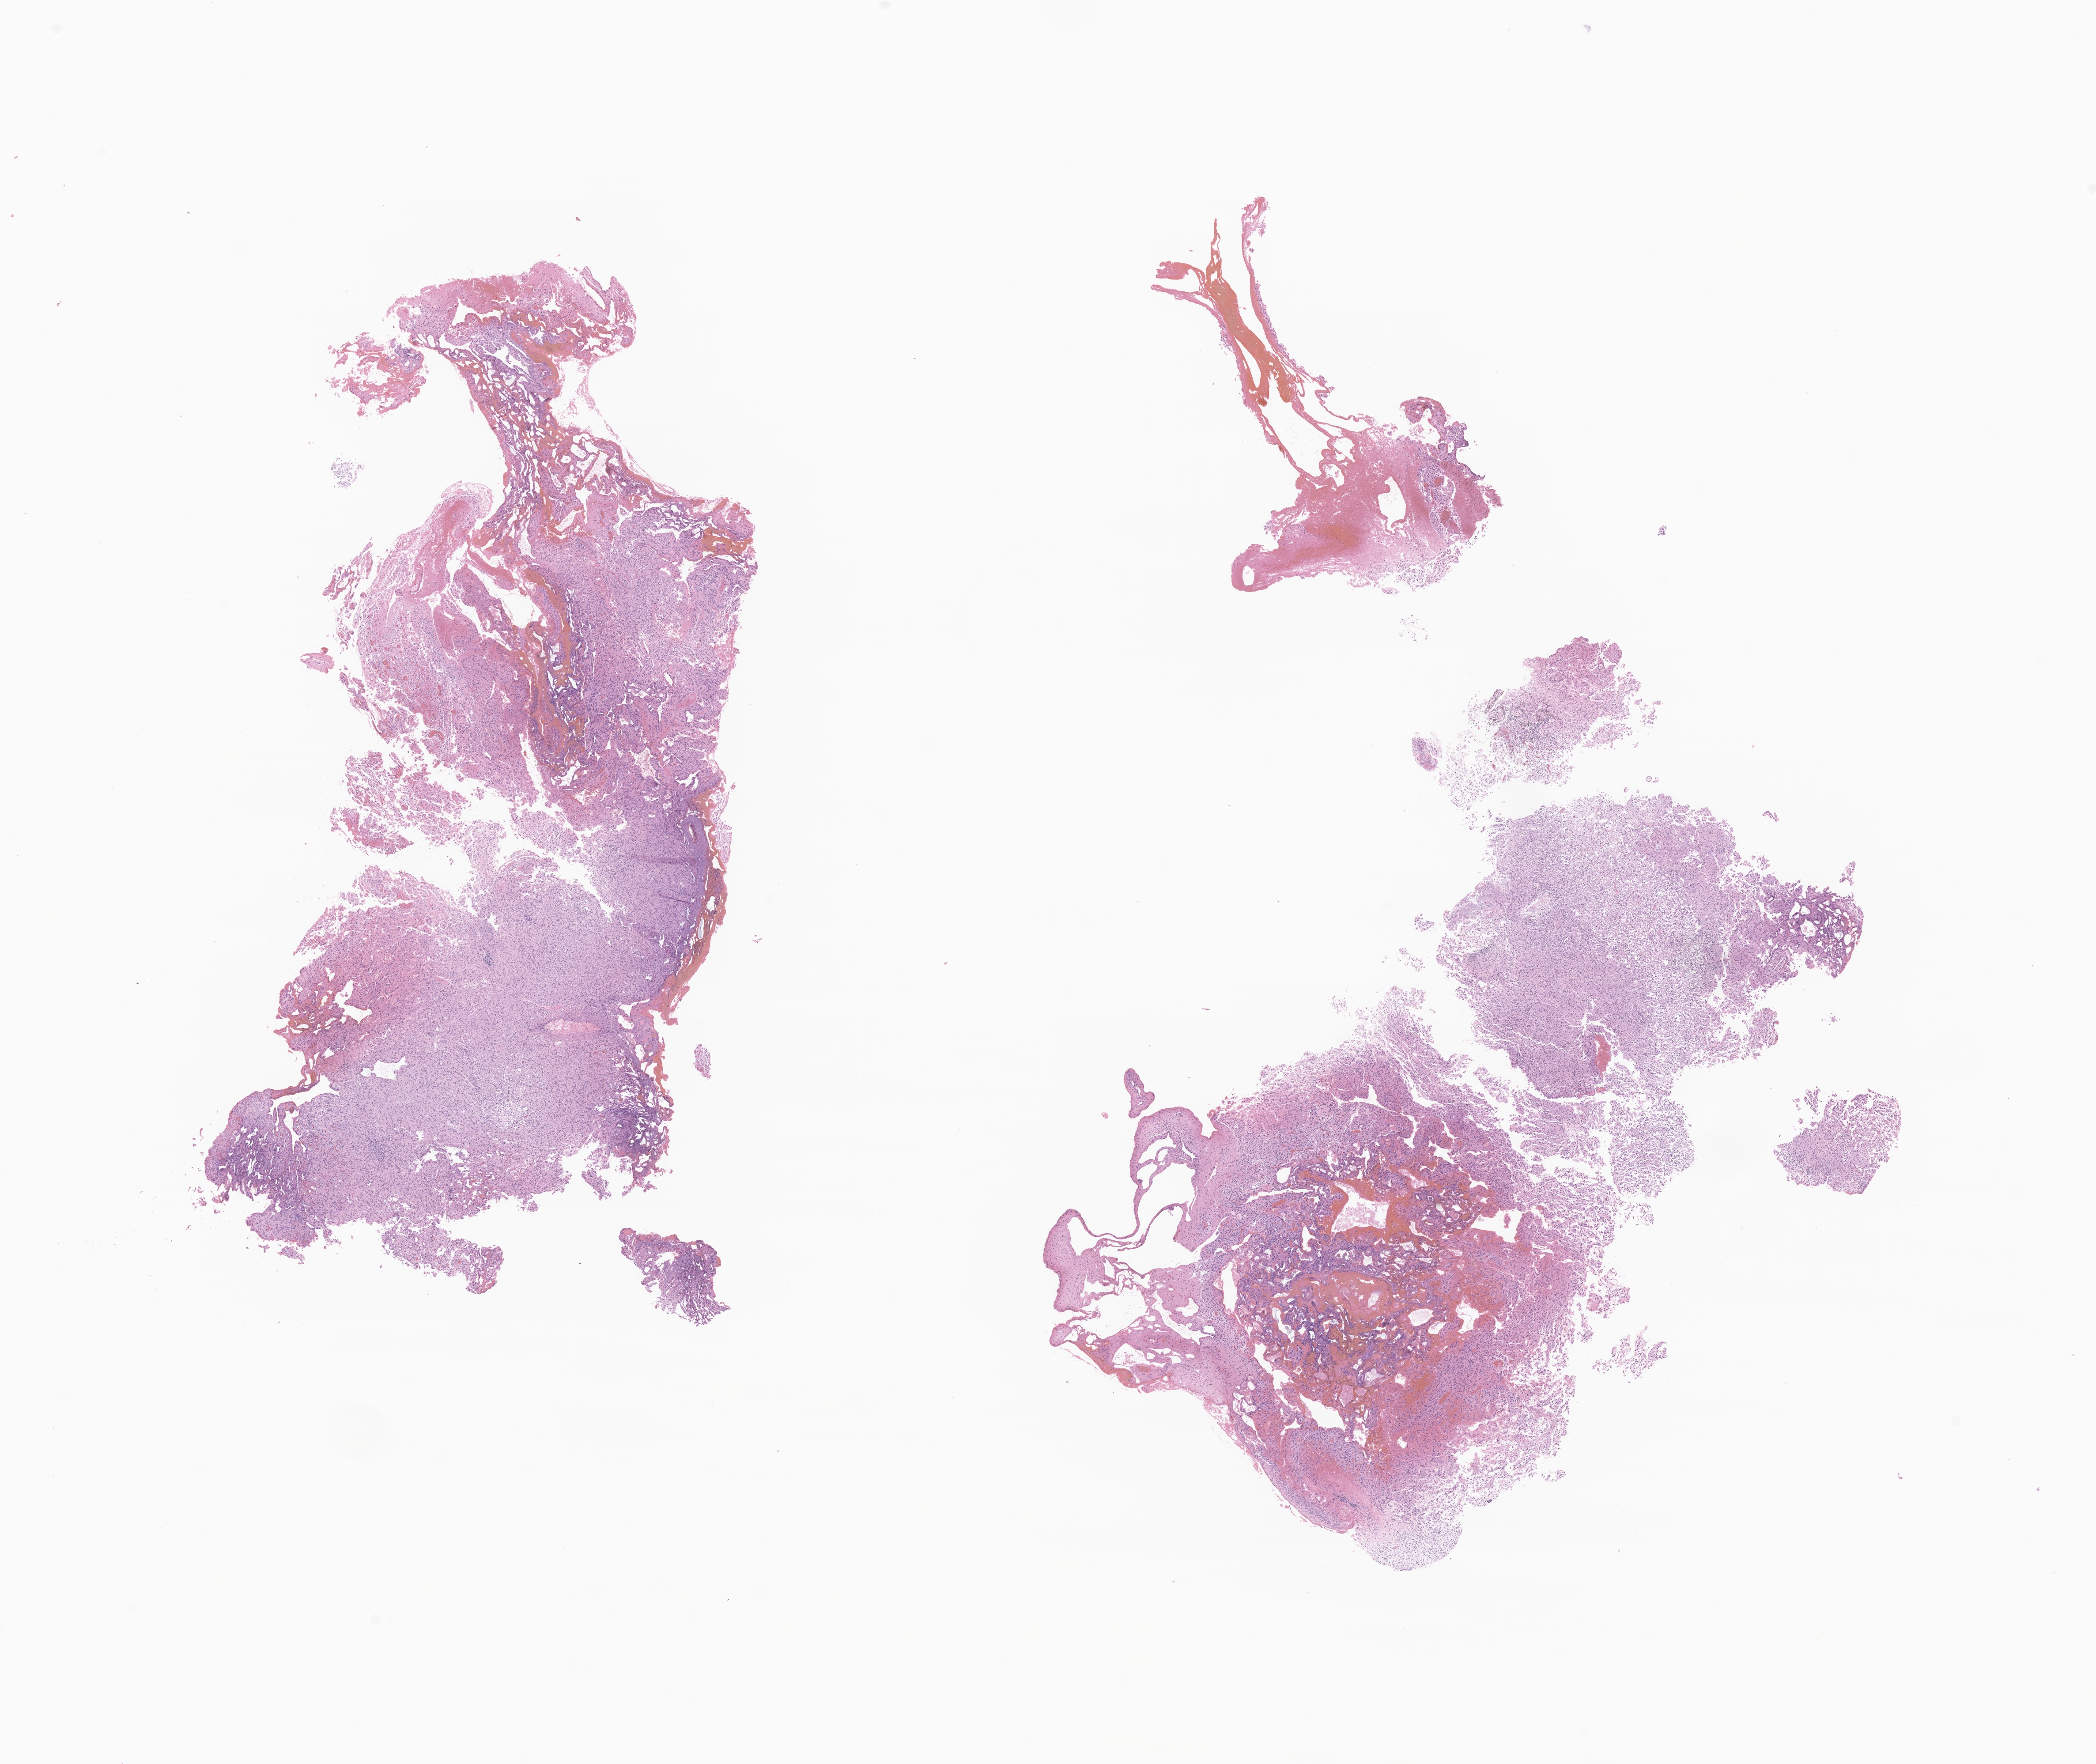
Whole-slide image, hematoxylin and eosin (H&E) stain of tumor tissue from the brain — a low-resolution overview of the entire scanned area, about 20.0 x 16.8 mm. FFPE section. Patient: female, age 46 months (3 years 10 months).
Recorded diagnosis: Pineocytoma.